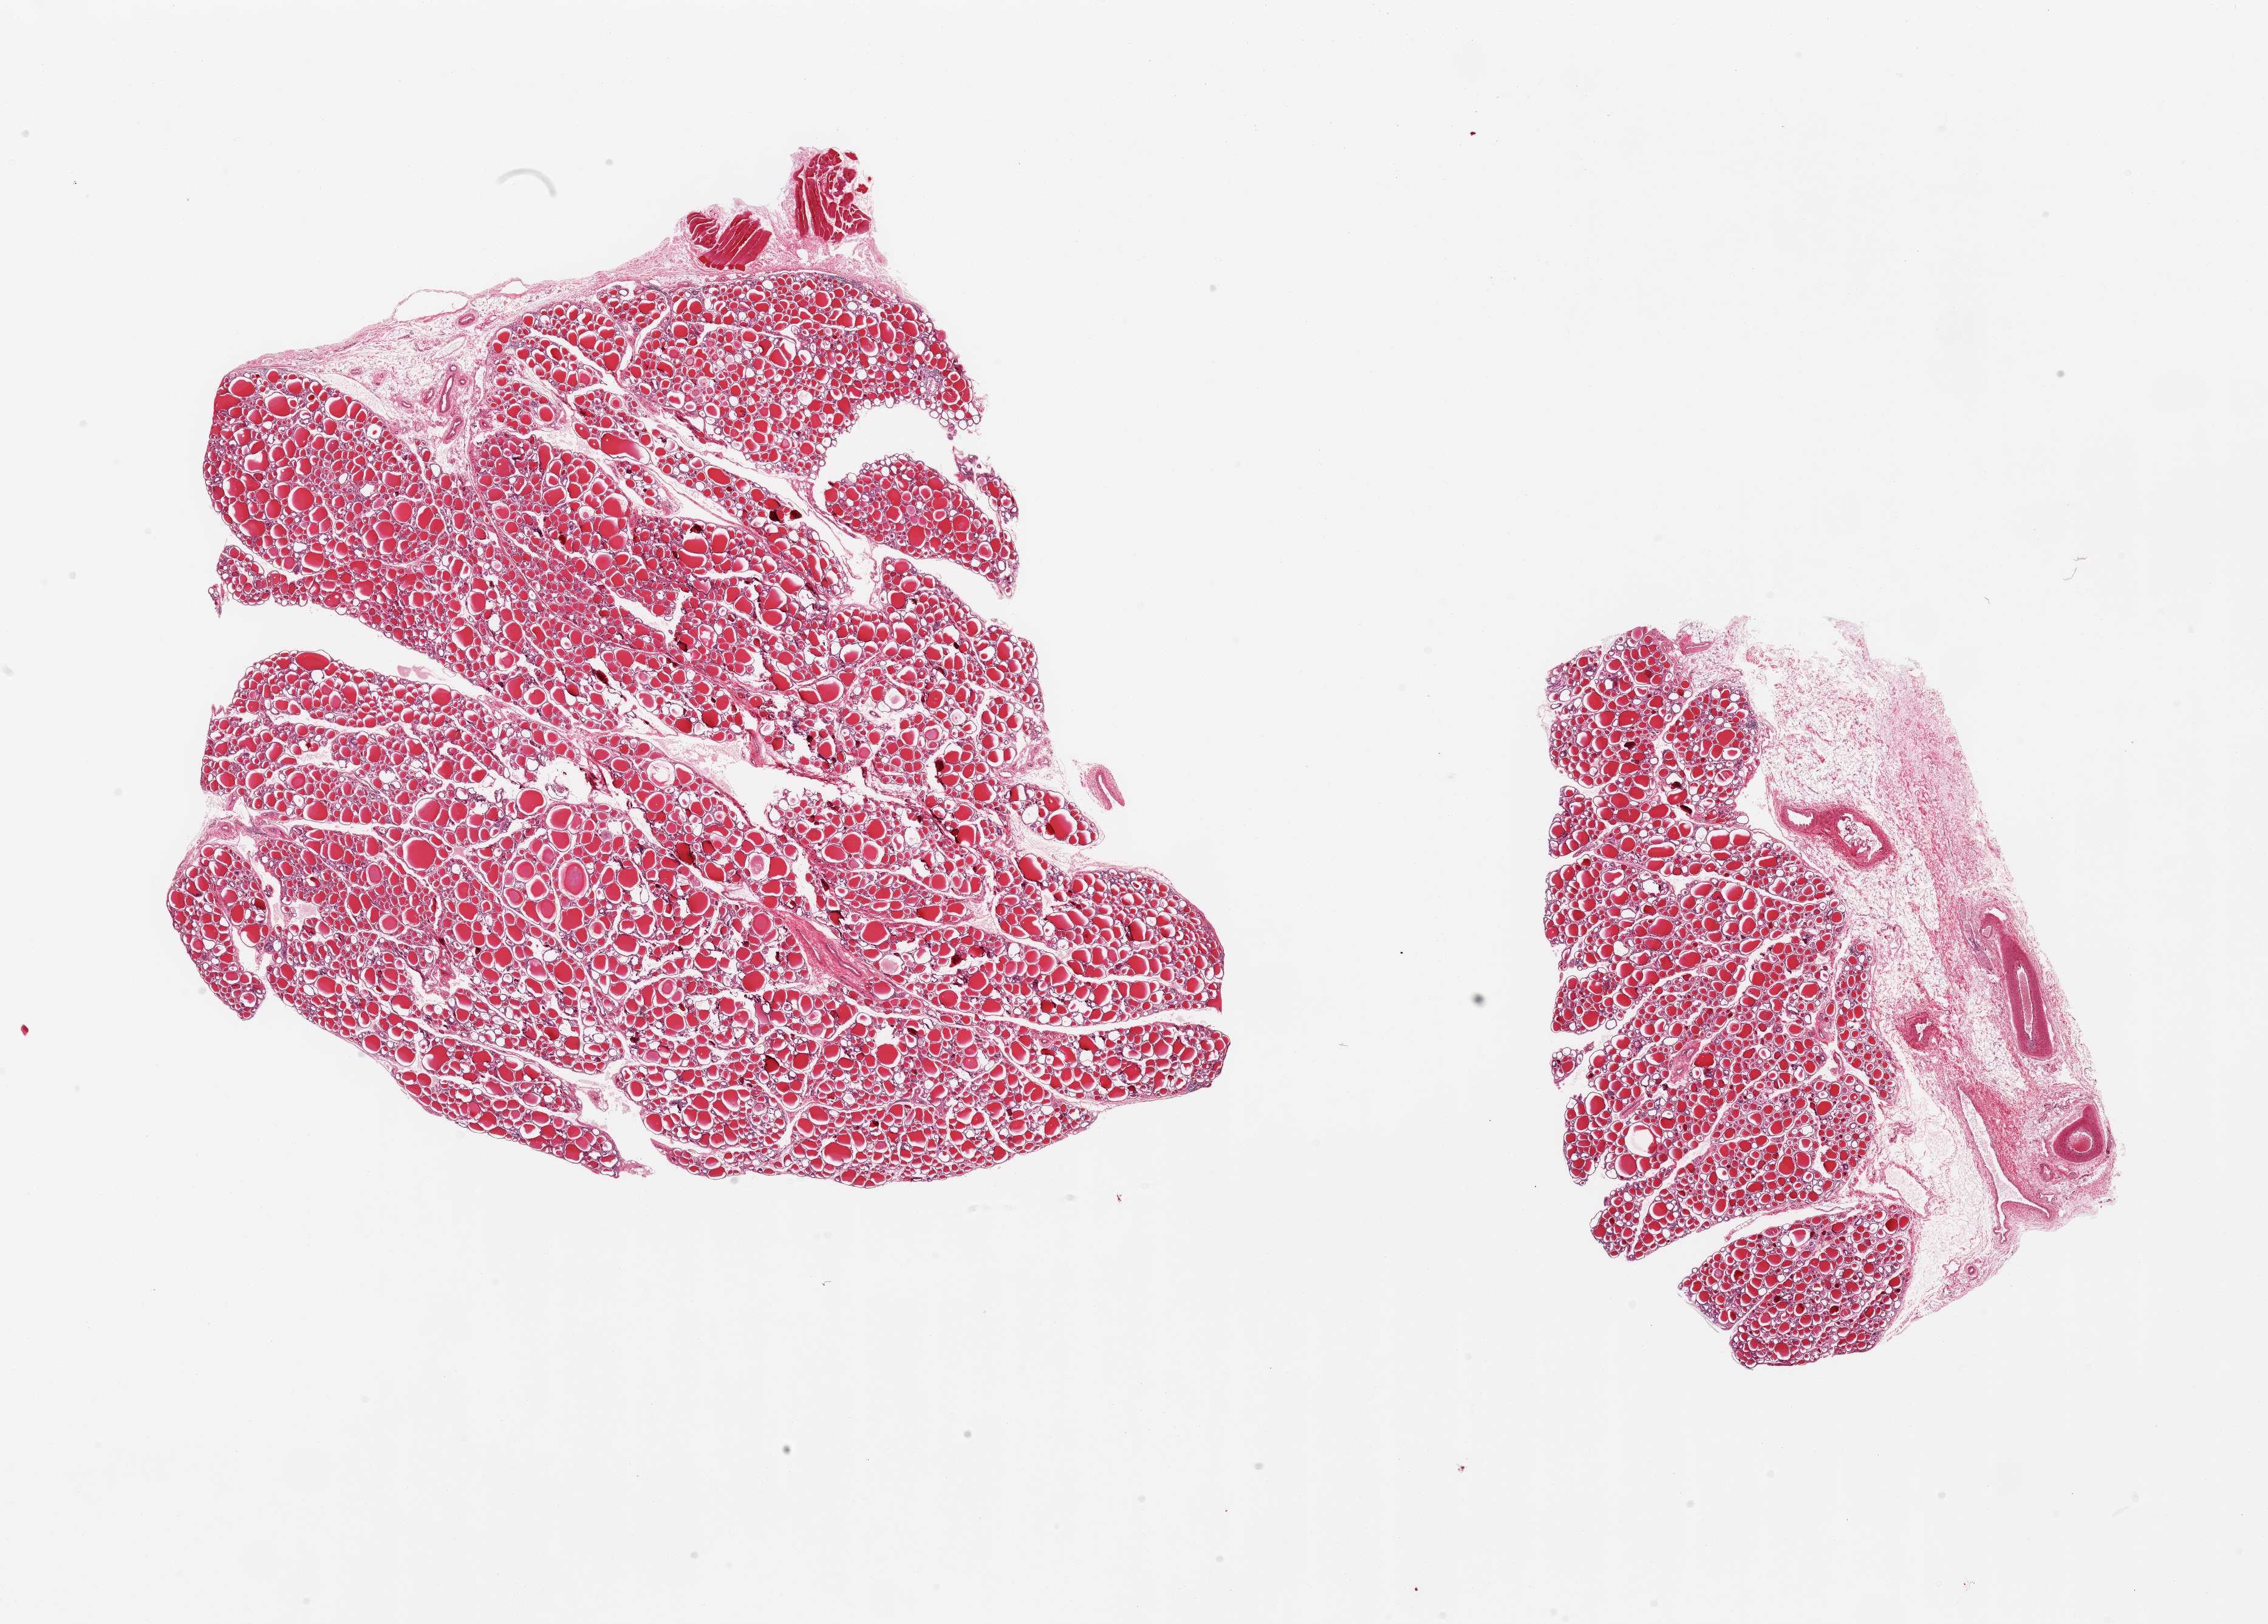
Whole-slide image, haematoxylin and eosin stain, brightfield — a low-resolution overview of the entire scanned area, about 29.5 x 21.1 mm (from a 20x scan); PAXgene-fixed paraffin-embedded (PFPE) section; target tissue: thyroid; tissue donor sample. Donor: male.
Reviewer comment on this tissue sample: 2 pieces; one is up to 30% fat/vessels, second includes smaller portion of fat/vessels/skeletal muscle.